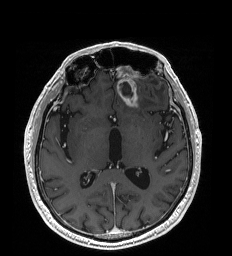
Brain MRI from a brain-tumour surgery series, one axial slice. Position 104 of 192 along the scan axis. T1-weighted post-contrast. 232 × 256 image matrix. From the clinical record (not read from this slice): histopathology: Glioblastoma; WHO grade: 4; IDH mutation: no.
Outlined on this slice (manually delineated by an expert):
- tumour: bounding box (x1, y1, x2, y2) in pixels: (120, 84, 138, 107)